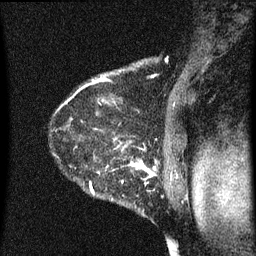
Breast MRI (dynamic contrast-enhanced), one sagittal slice. Slice 52 of 60 in the series (ordered by position). Dynamic contrast-enhanced series, image 2 of 3 at this slice position (ordered by acquisition). 1.5 T. TE 4.2 ms, TR 8 ms. 2 mm slice thickness. 256 × 256 image matrix. Female patient, age 54 years.
Outlined on this slice (semi-automatically segmented with operator editing):
- analysis volume of interest (the breast-tissue region the enhancement analysis was run in; not a lesion): bounding box [x1, y1, x2, y2] px = [49, 138, 164, 209]
- tumour enhancement mask (voxels above the 70 % enhancement threshold inside the analysis volume of interest): [74, 138, 156, 195]